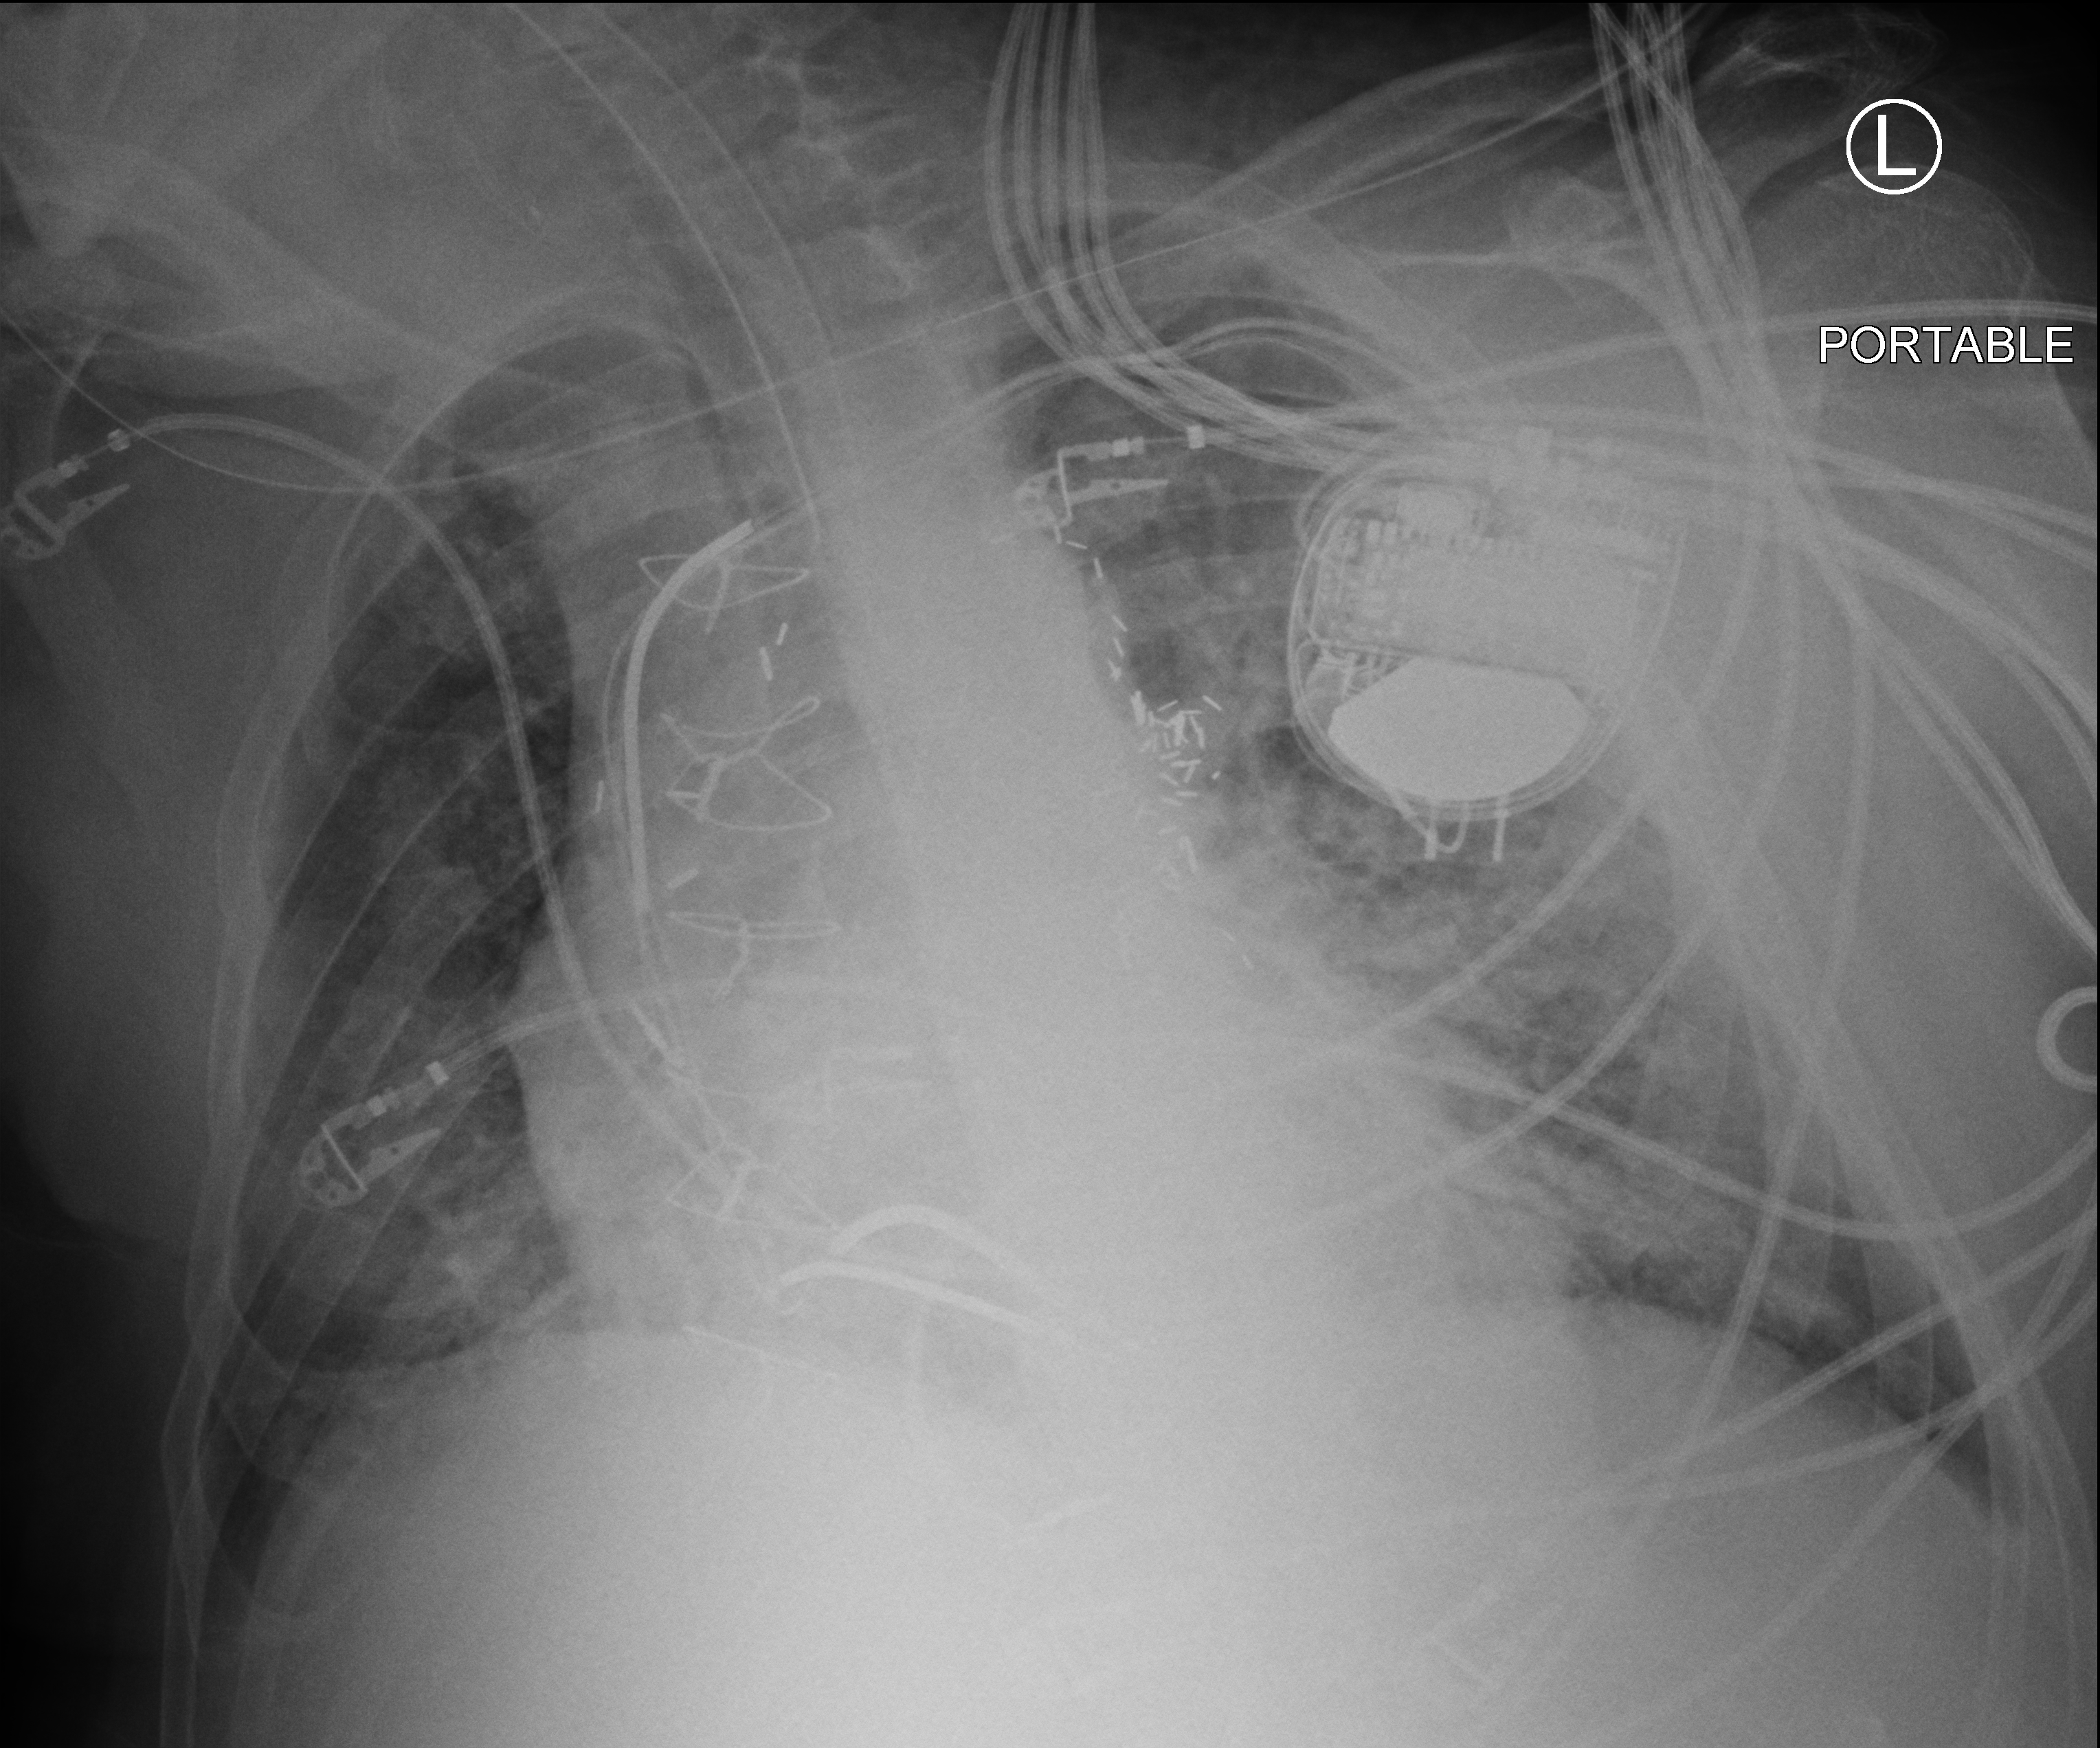
Chest X-ray (portable); anteroposterior (AP) projection. Patient hospitalised with COVID-19; male, aged 60–74 years.
Hospital-stay facts (about this admission, not read from this image; timing relative to this image not recorded): admitted to intensive care during this hospital stay: yes; smoking status (admission record): never; length of hospital stay: 55 days.